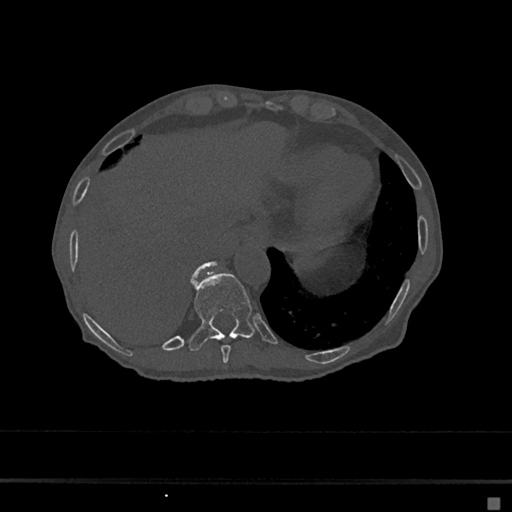
CT including the spine, one axial slice. Reconstruction kernel Br40s/3. 120 kVp. Bone window (W 1800 / L 400 HU). 512 × 512 image matrix. Patient: female, 68 years. Case-level facts recorded for this patient, not image findings: primary cancer: renal.
Annotated regions visible in this slice (semi-automatically segmented with operator editing):
- T10 vertebra: box from (x=189, y=273) to (x=256, y=351) px
- T11 vertebra: (x=192, y=261)–(x=217, y=279)
- T9 vertebra: (x=221, y=345)–(x=231, y=363)